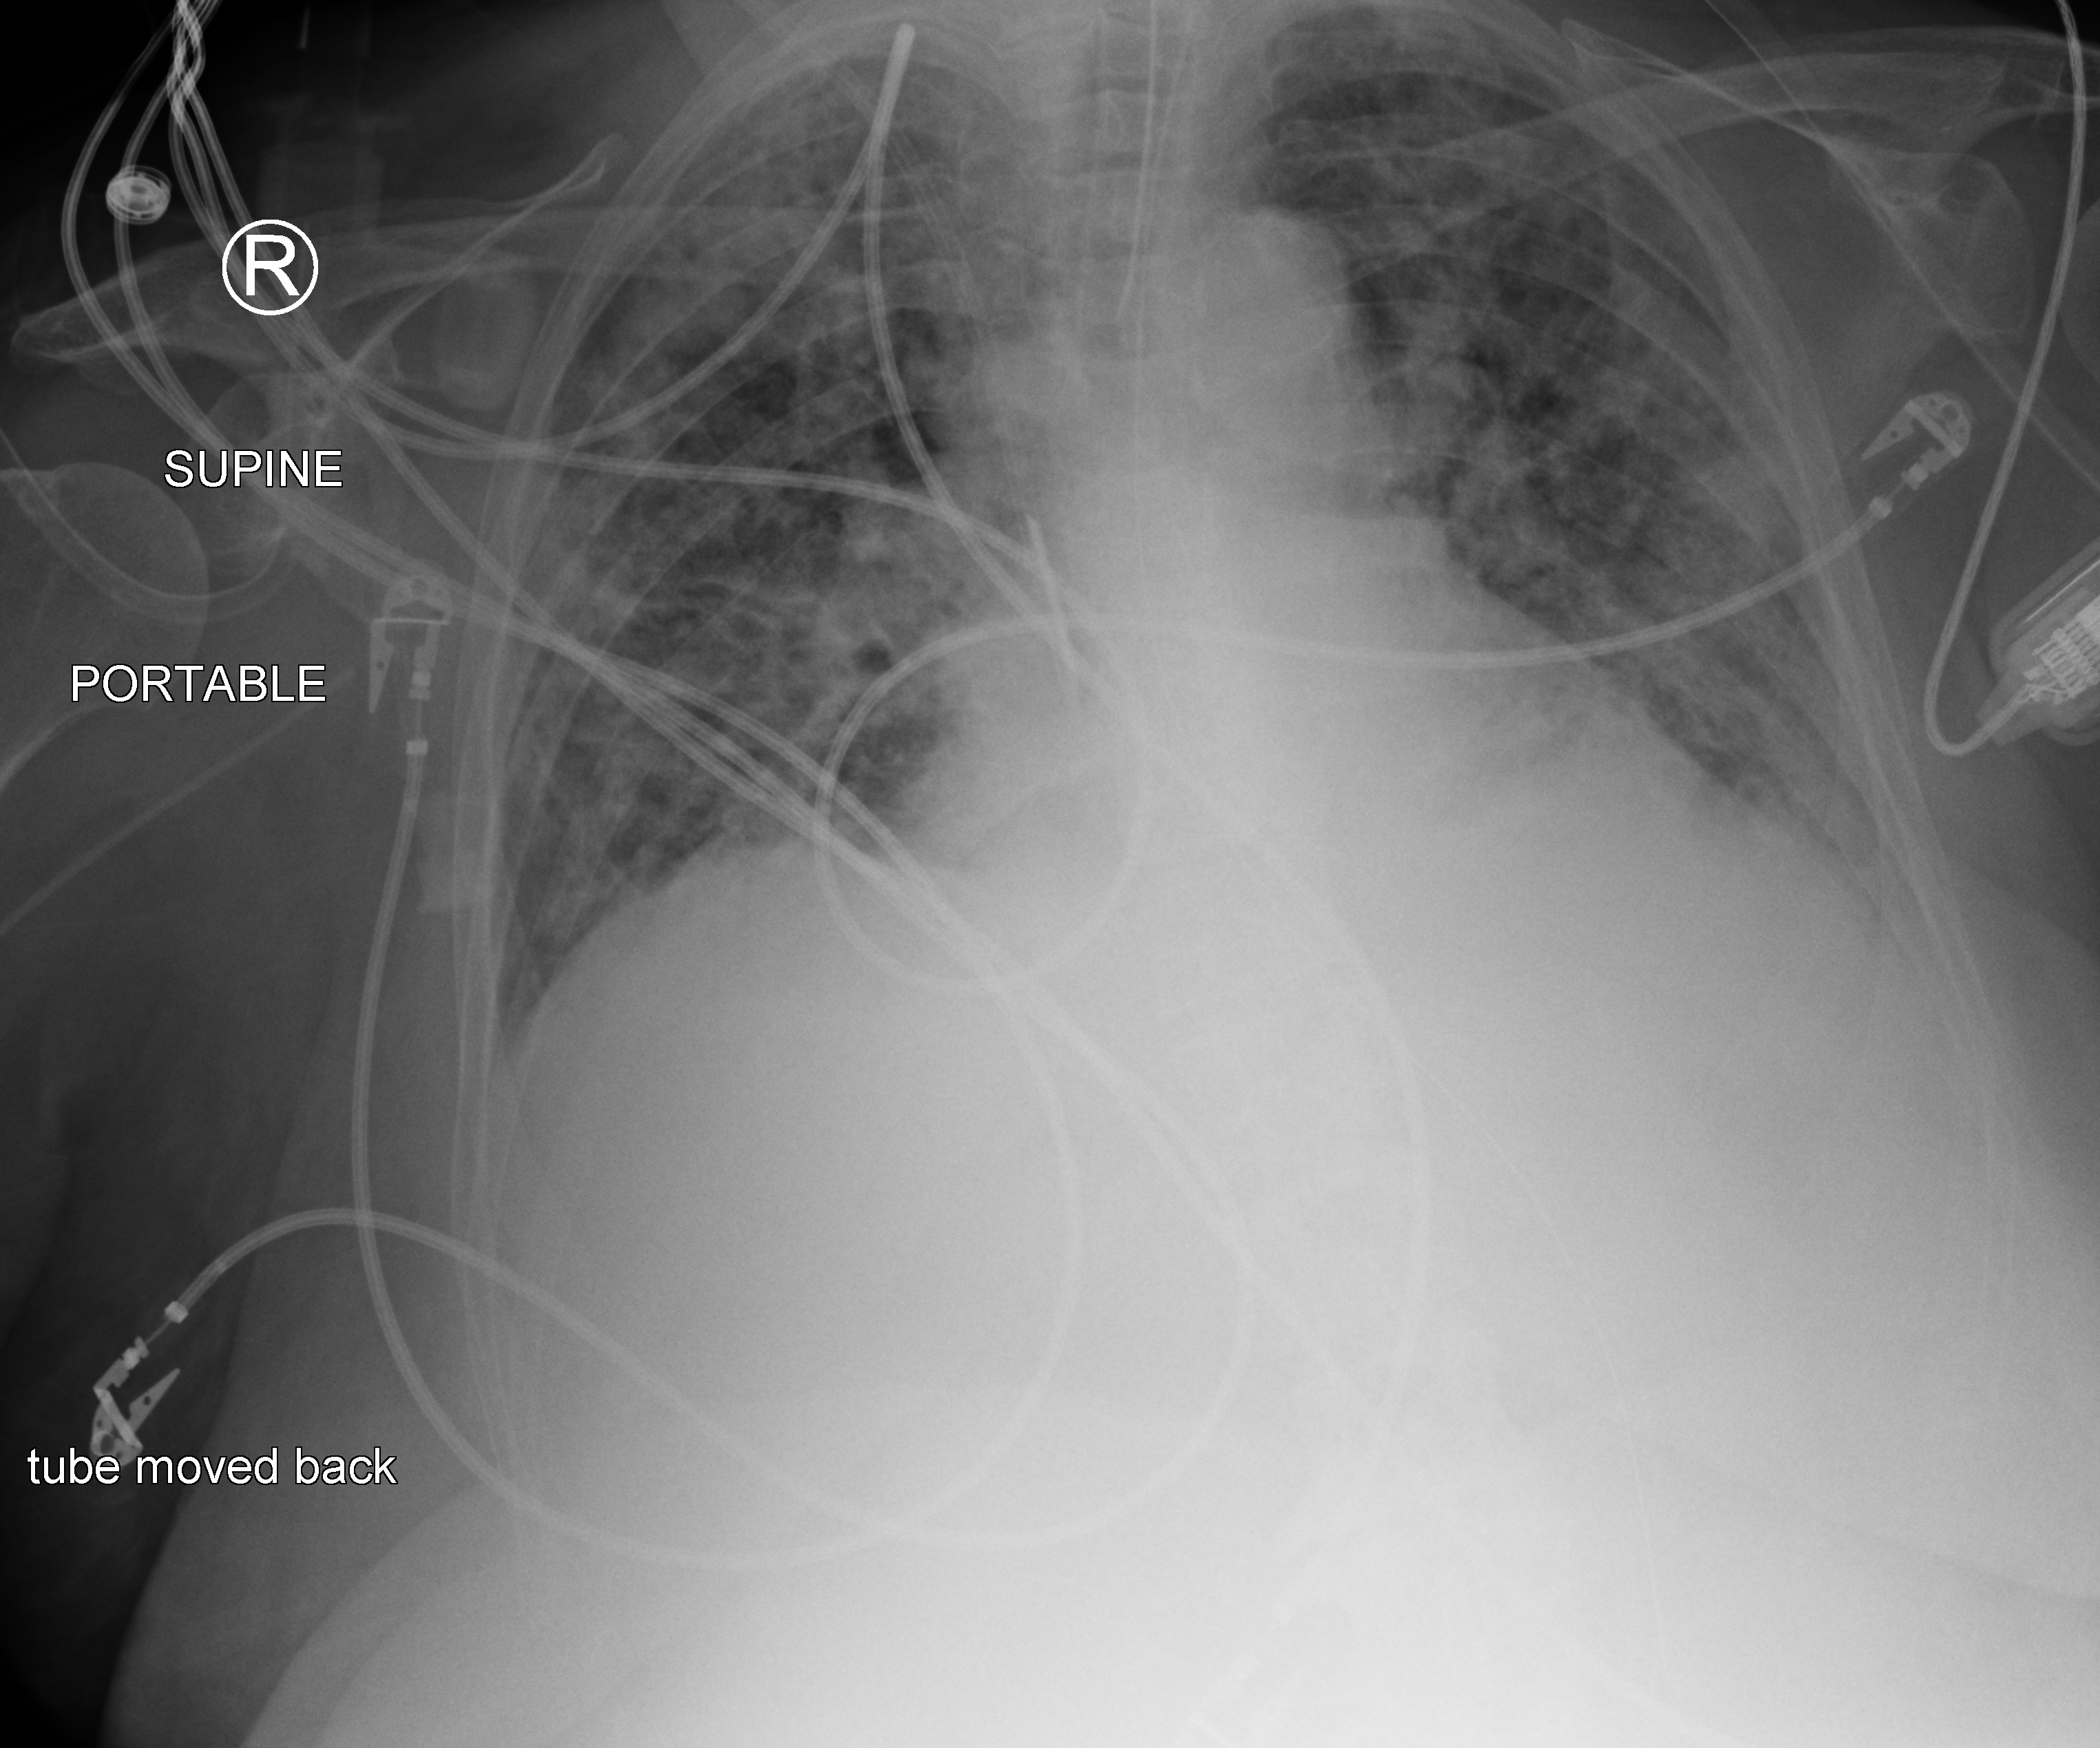
Portable chest radiograph; anteroposterior (AP) projection. Patient hospitalised with COVID-19; female, aged 75–90 years.
From the hospital-stay record, not from the radiograph (when in the stay this image was taken is not recorded):
- diabetes (admission record): no
- smoking status (admission record): former
- mechanically ventilated during this hospital stay: yes